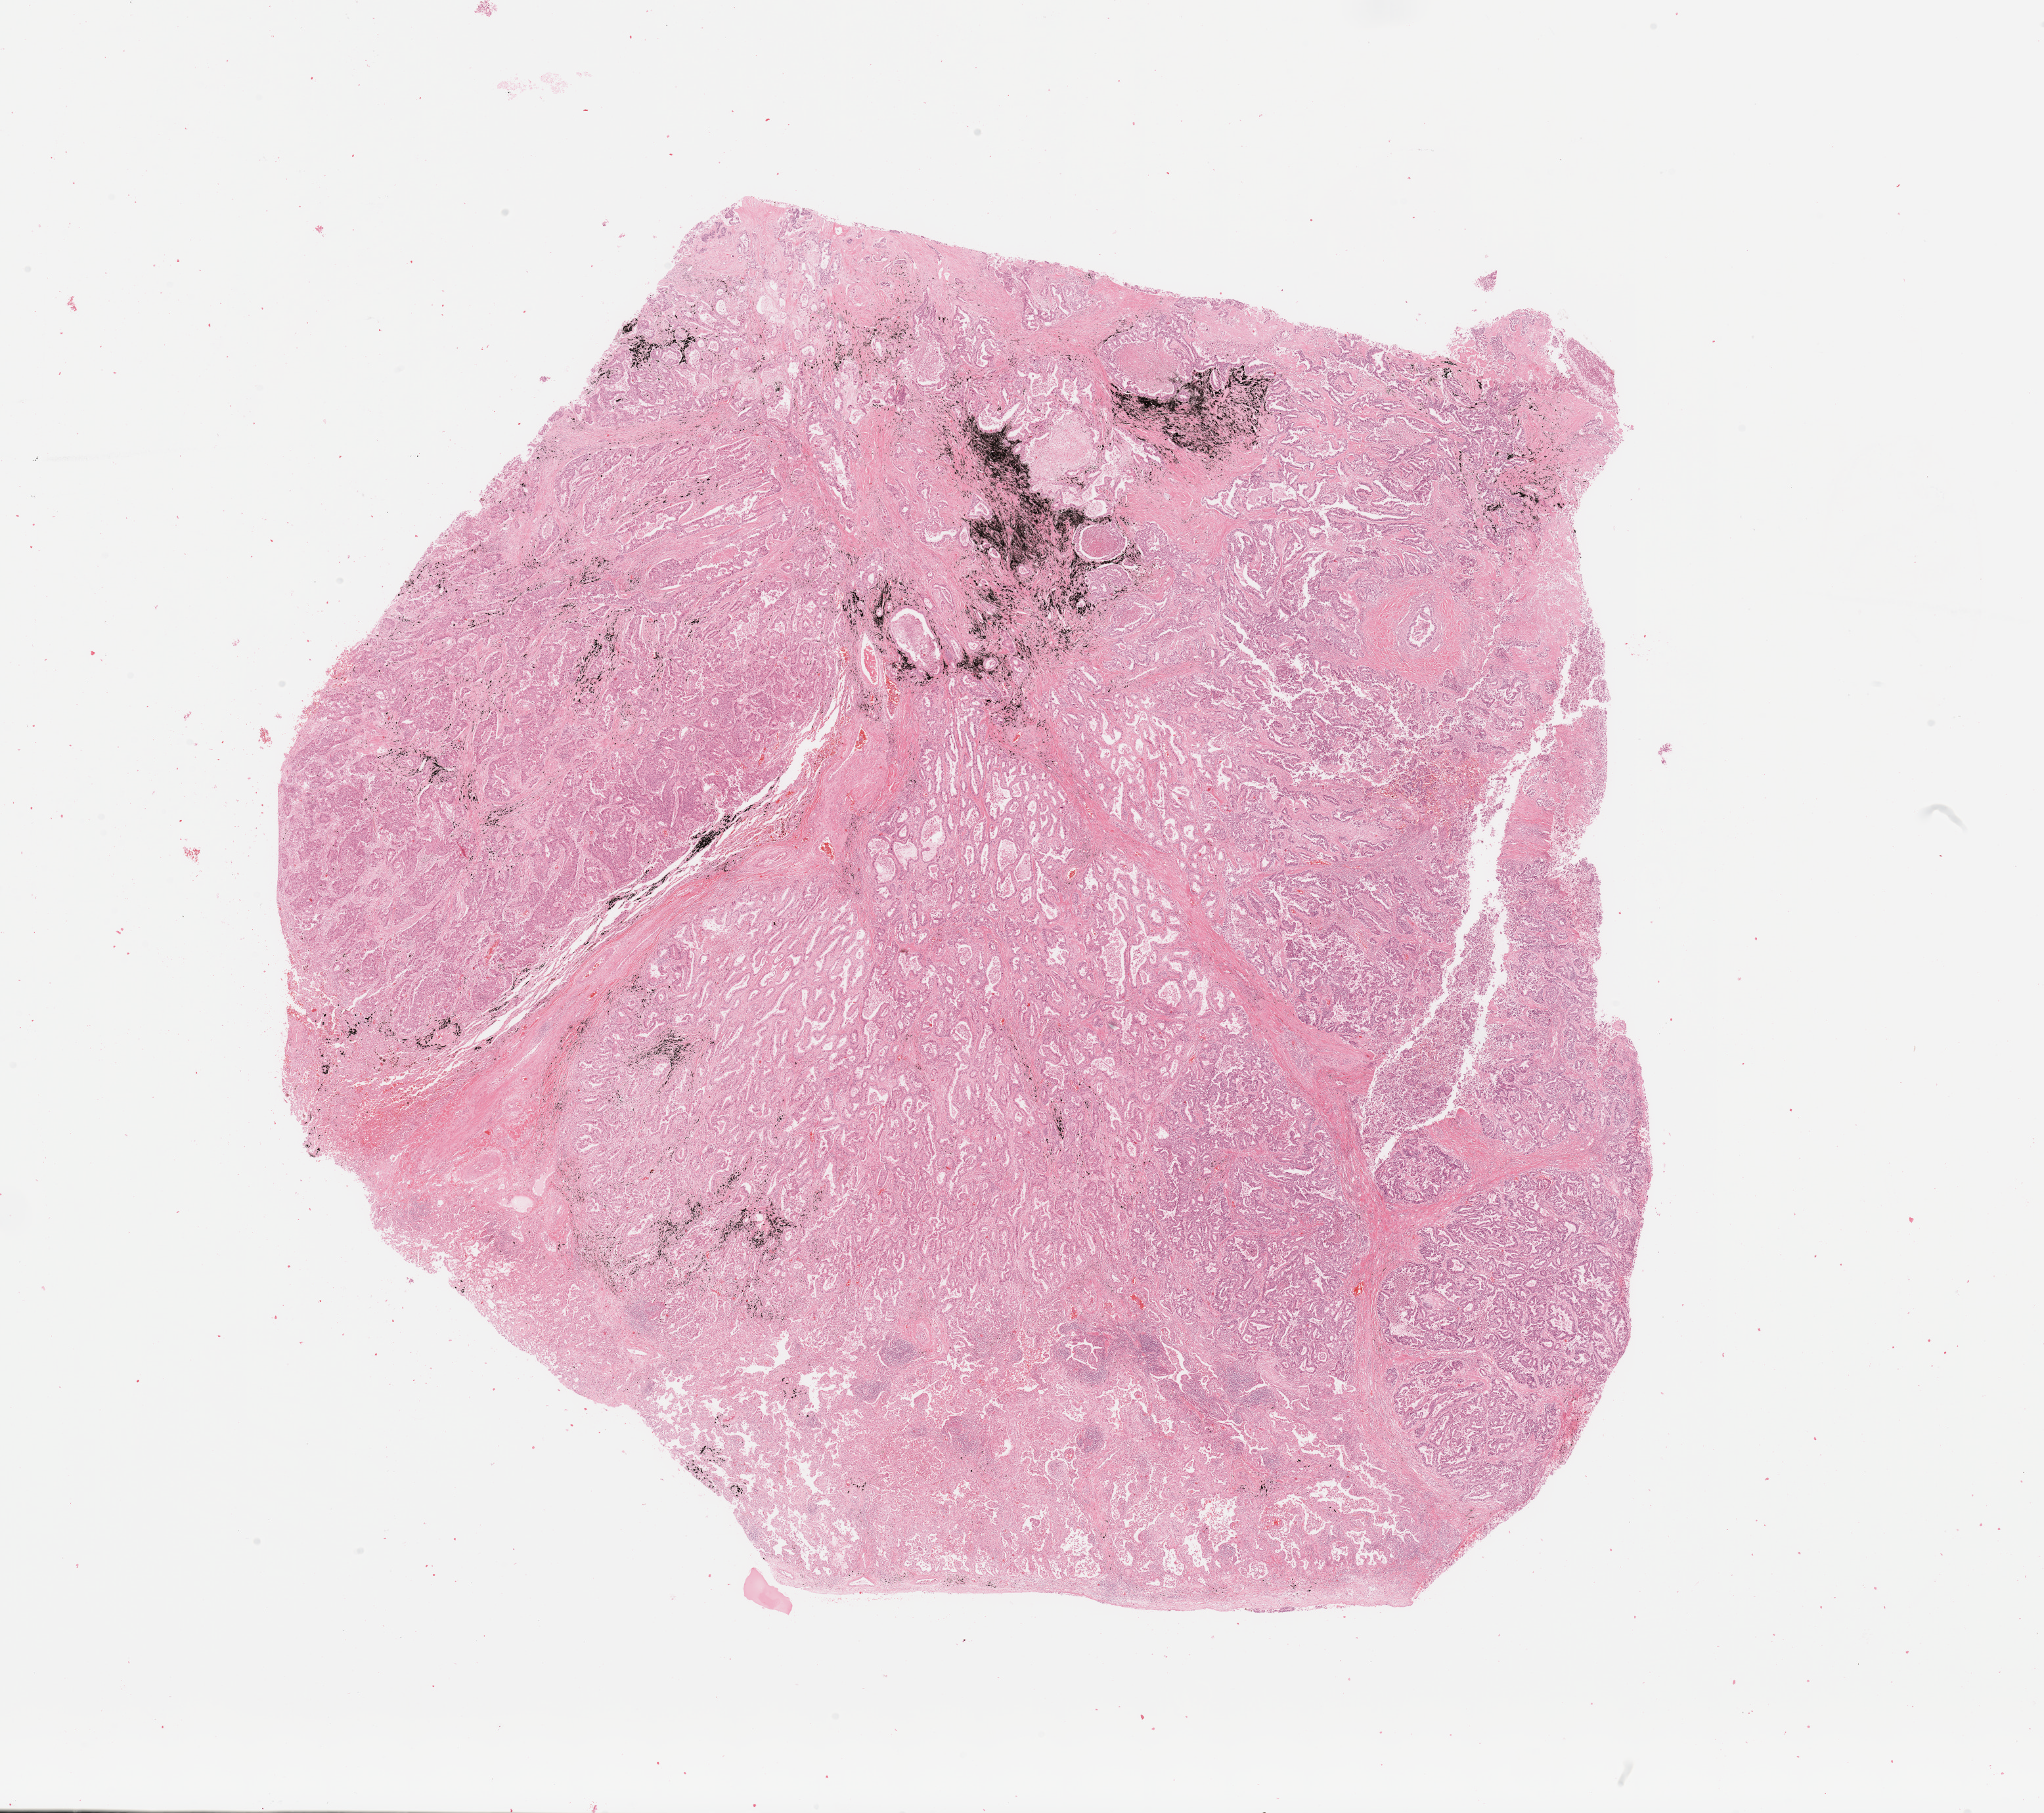
Whole-slide histology image, H&E — low-resolution overview of the scanned area, about 24.6 x 21.8 mm (slide scanned at 20x); tumour tissue sample, lung. 56-year-old male patient.
Diagnosis: Adenocarcinoma, NOS.